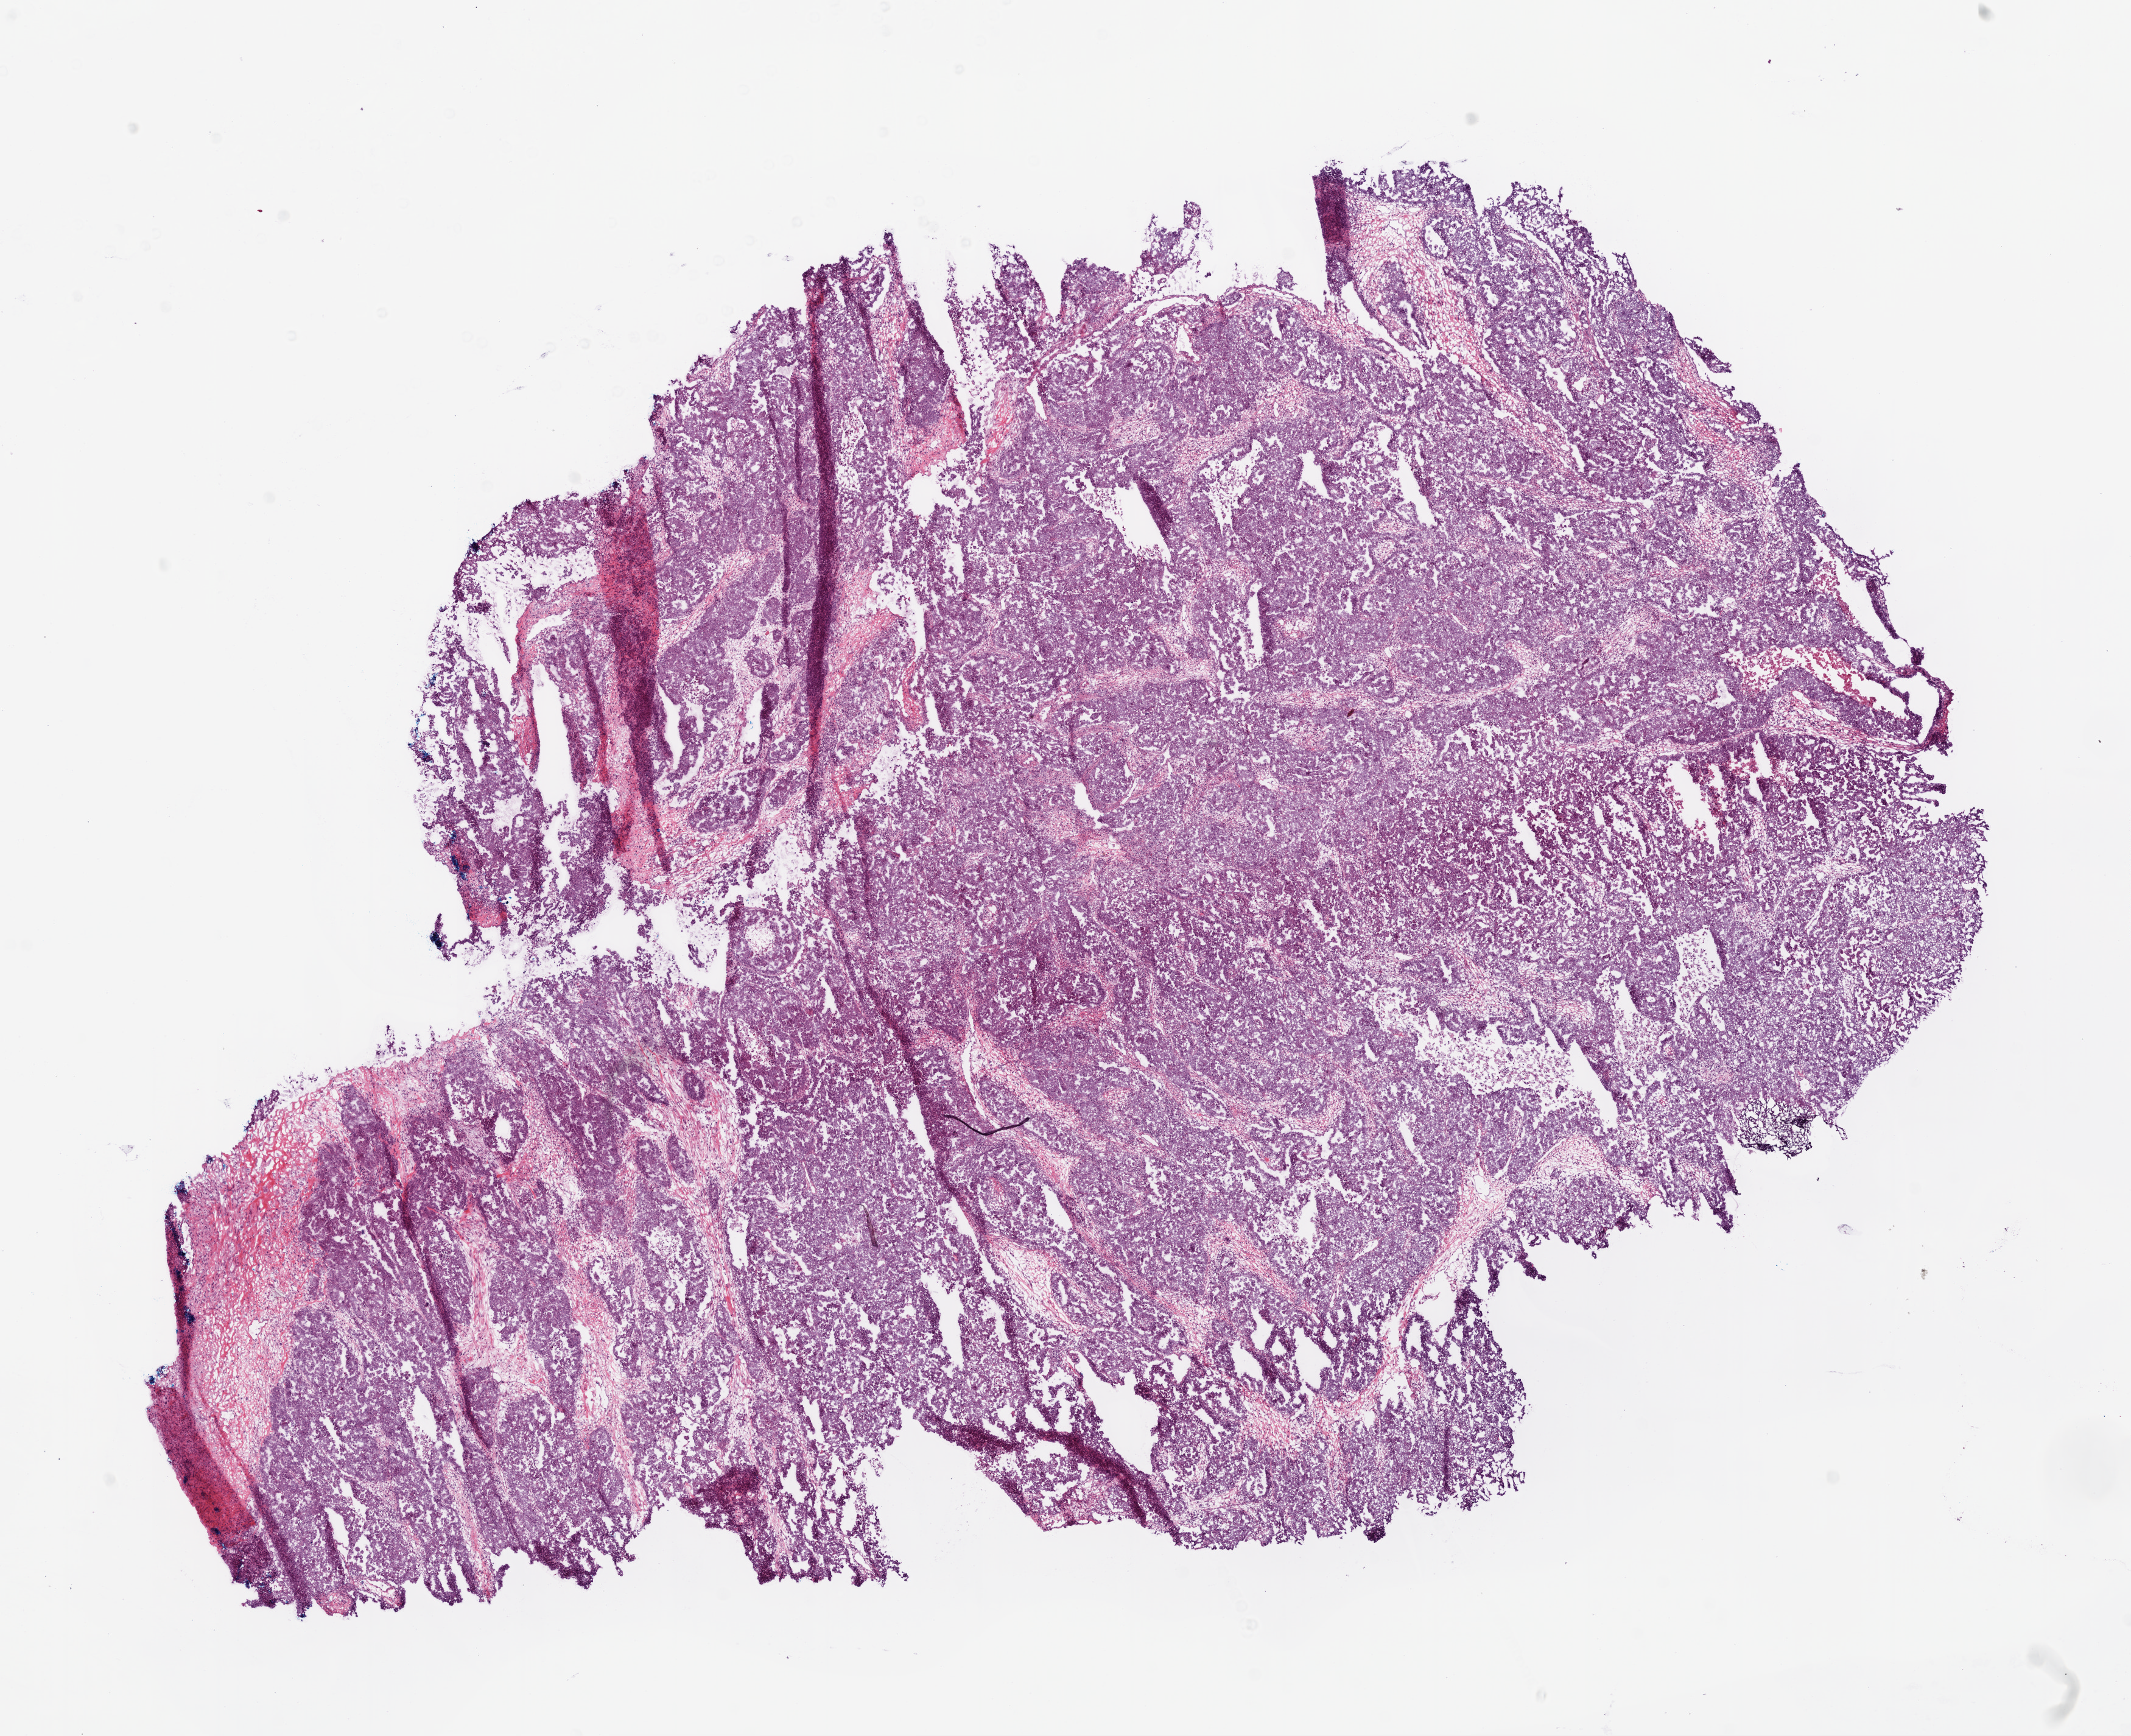
Digitized H&E-stained tissue section (whole slide), low-resolution overview of the scanned area, about 14.0 x 11.4 mm (slide scanned at 20x). Frozen section. Sample: primary tumour, ovary. Female patient; age at initial diagnosis 54 years. Histologic grade: G3 (poorly differentiated). Composition of this section per pathologist review: tumour cells 85%, tumour nuclei 90%, normal cells 0%, stromal cells 15%, necrosis 0%.
• FIGO stage: IIIC
• diagnosis: Serous cystadenocarcinoma, NOS